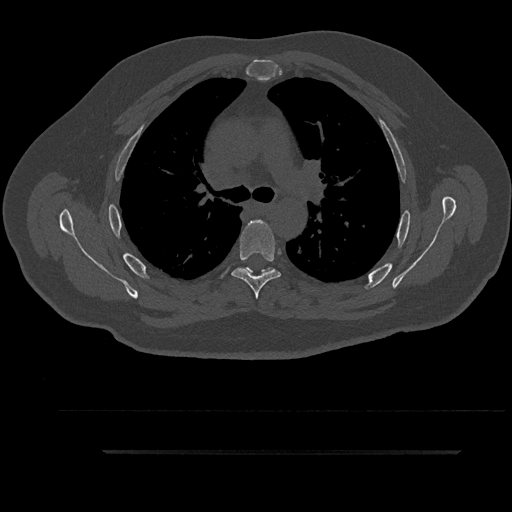
CT including the spine, one axial slice; position 625 of 797 along the scan axis; reconstruction kernel Br40s/3; 120 kVp; bone window (W 1800 / L 400 HU); 0.5 mm slice thickness; 512 × 512 image matrix, field of view 432 × 432 mm. Male patient, age 63 years. Case-level facts recorded for this patient, not image findings: primary cancer: renal; vertebrae with lytic lesions (as recorded): T8.
Structures marked on this image (semi-automatically segmented with operator editing):
- T5 vertebra: bounding box [x1, y1, x2, y2] px = [231, 220, 281, 299]
- T6 vertebra: [244, 267, 274, 276]